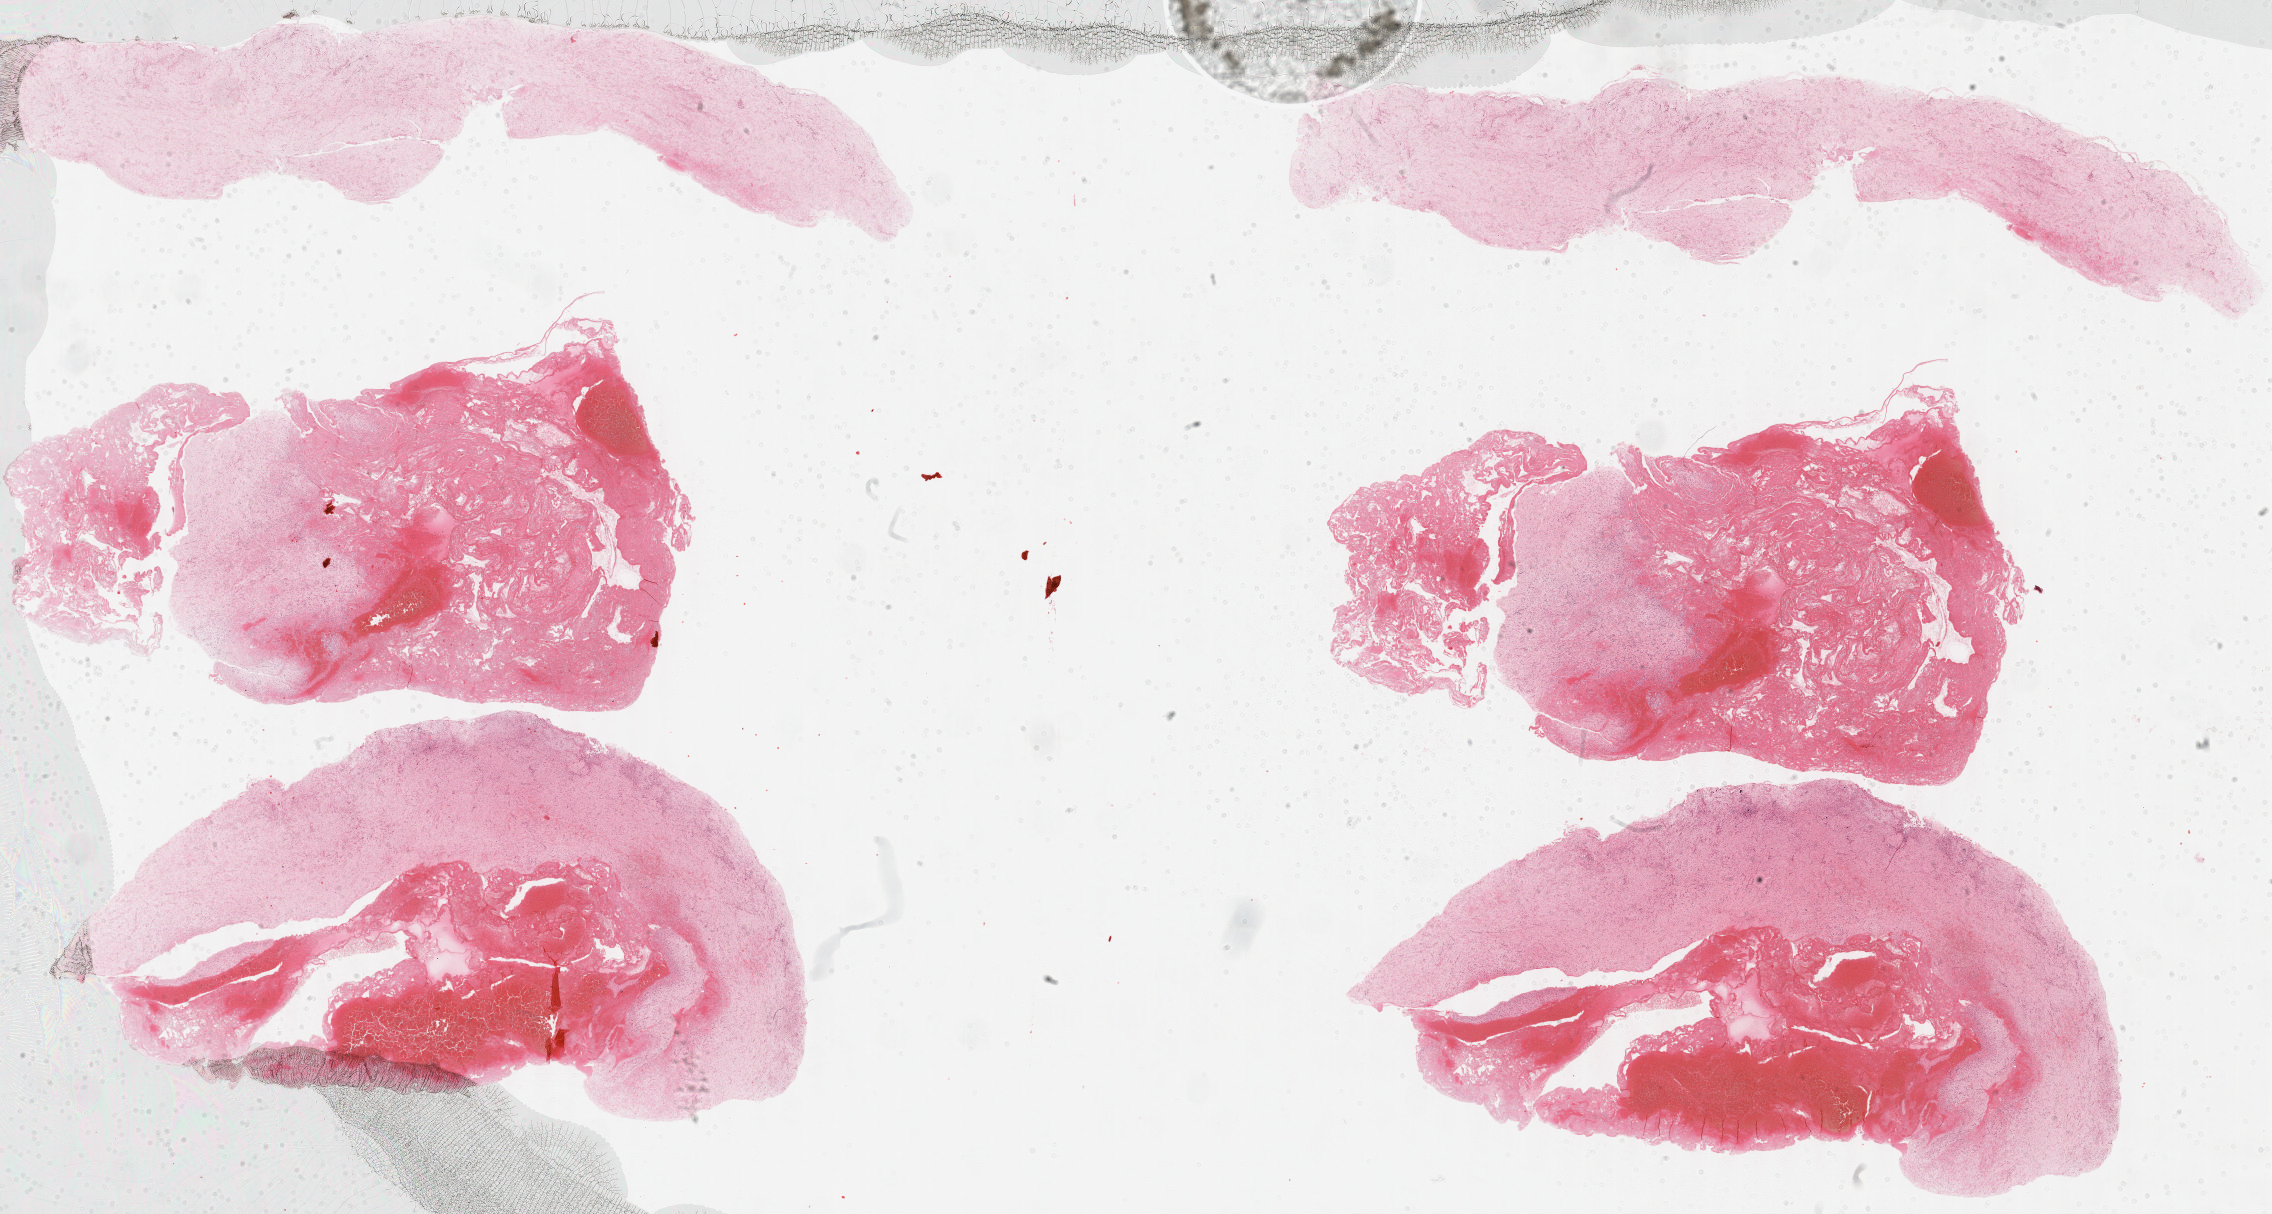
Whole-slide histology image, H&E, shown as a low-resolution overview of the whole scanned area (about 36.7 x 19.6 mm, from a 40x scan). Formalin-fixed paraffin-embedded (FFPE) diagnostic section. Primary tumour sample from the mesothelium. Female, age 81 years at initial diagnosis.
- pathologic diagnosis: Epithelioid mesothelioma, malignant (pleura, NOS)
- laterality: right
- AJCC pathologic stage: I